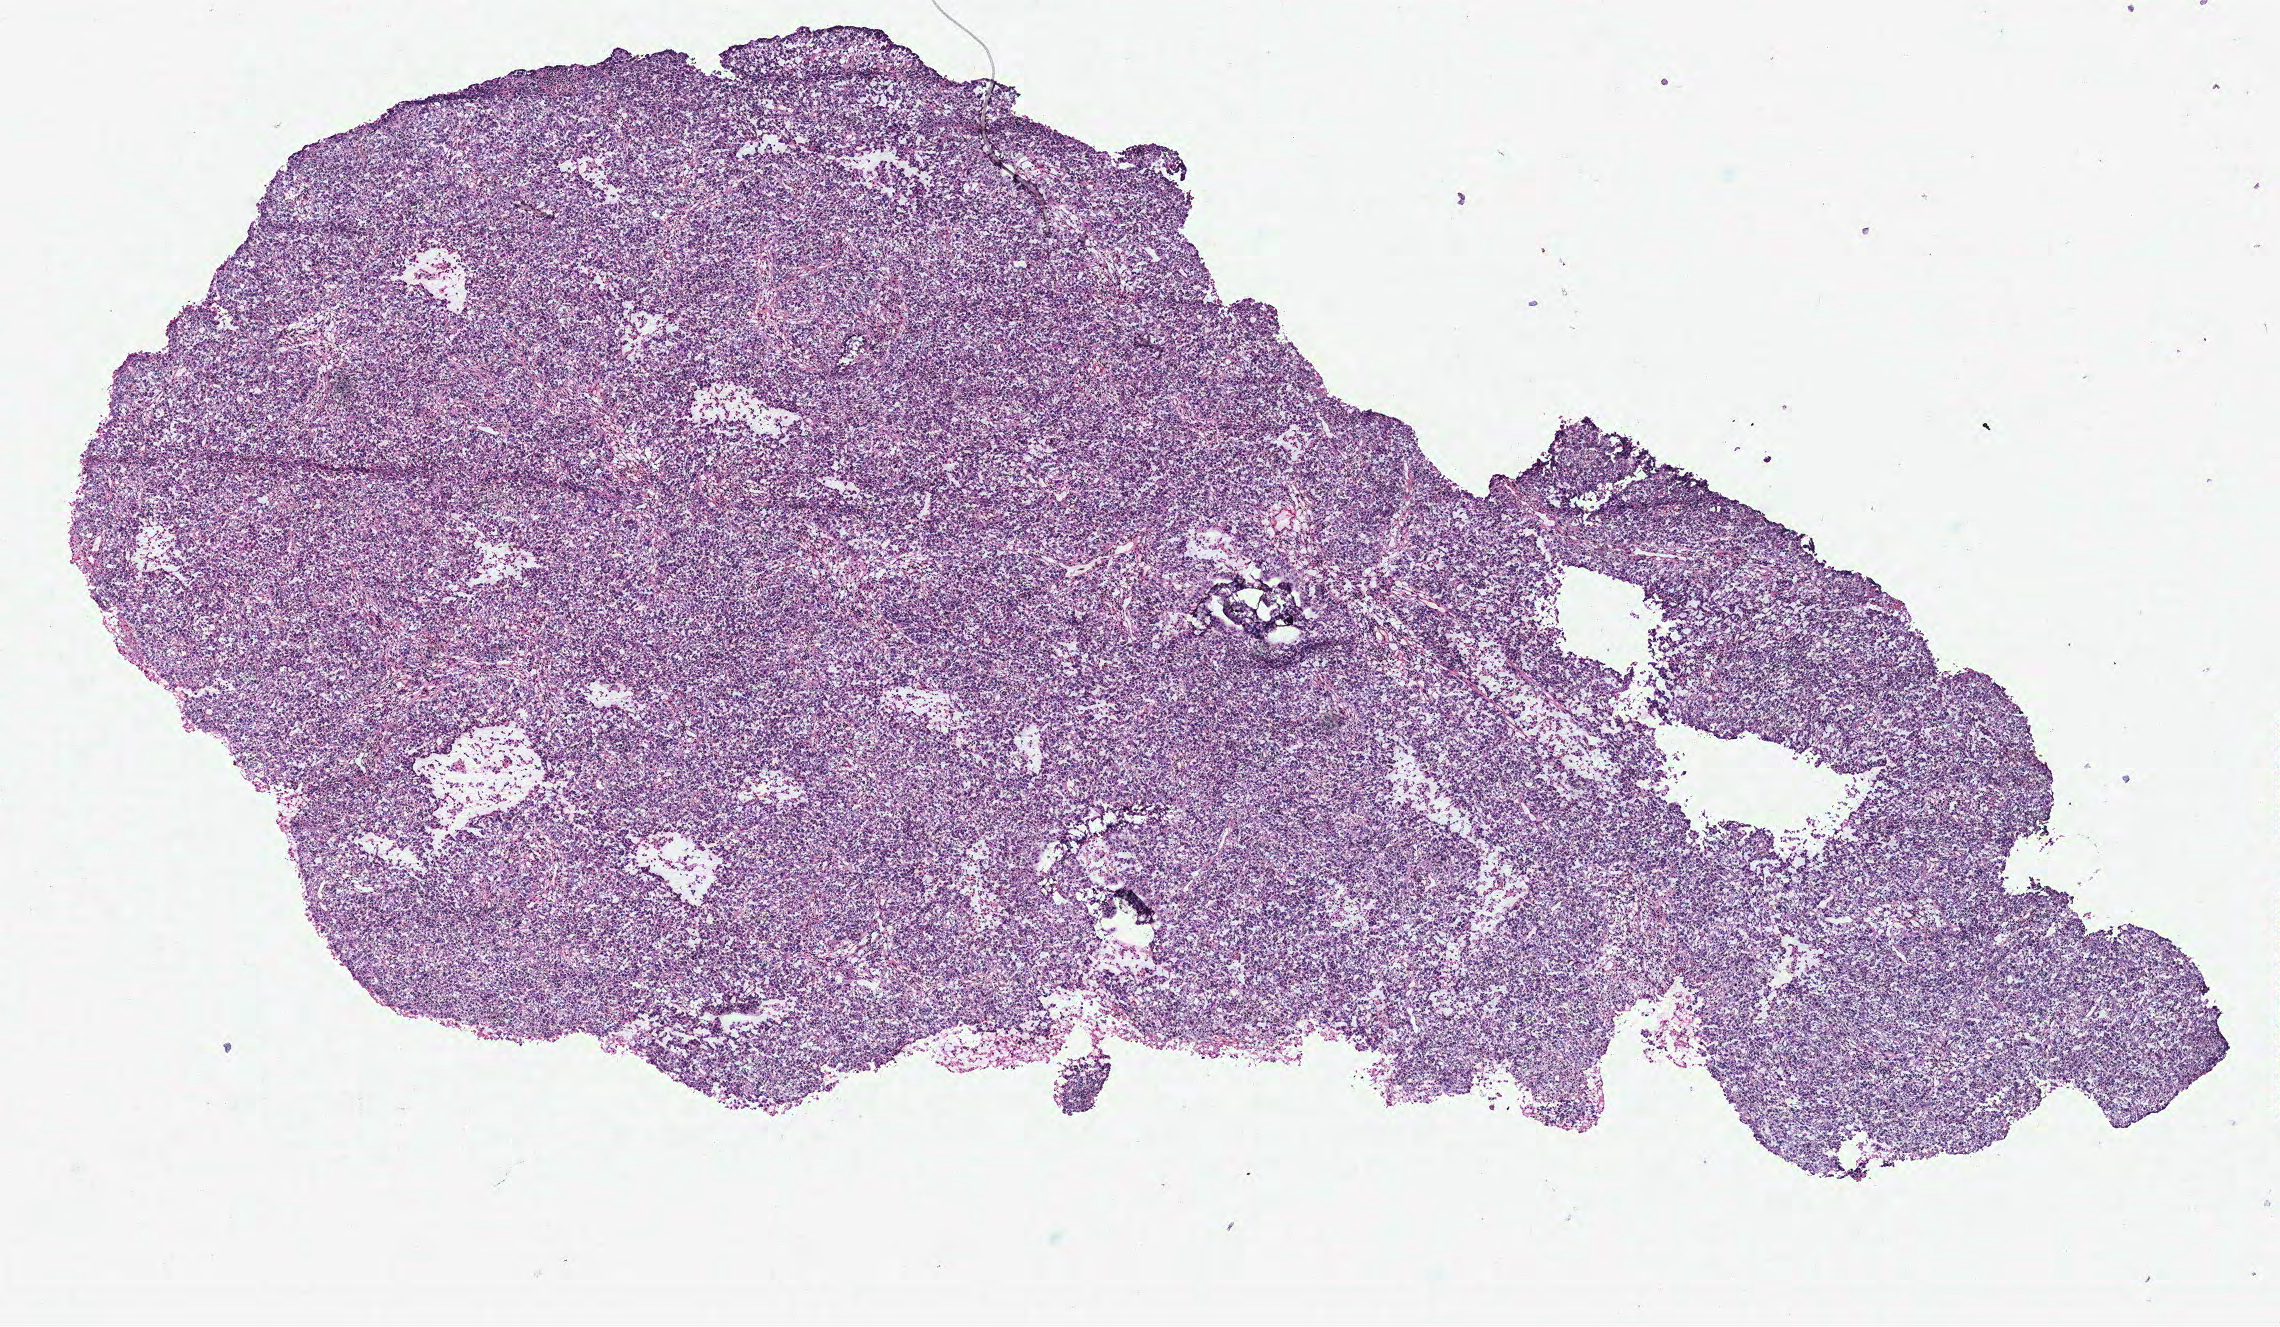
Digitized H&E-stained tissue section (whole slide) — whole scanned area (about 9.1 x 5.3 mm) shown as a low-resolution overview. Tumour tissue sample, breast. 61-year-old female patient.
- diagnosis: Infiltrating duct carcinoma, NOS
- AJCC pathologic stage: IIA